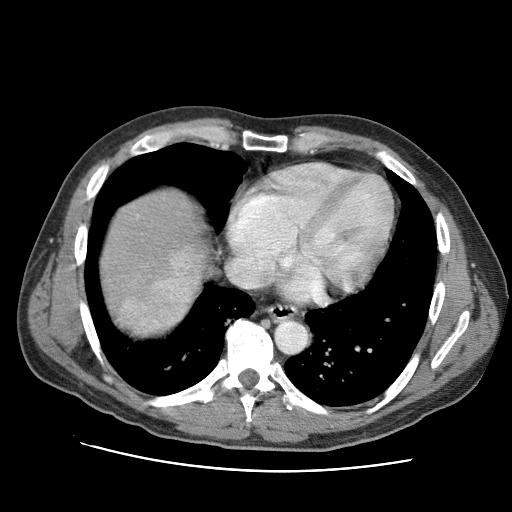
Contrast-enhanced abdominal CT (liver protocol), one axial slice; slice 88 of 95 in the series (ordered by position); reconstruction kernel STANDARD; 120 kVp; one of 2 acquisitions stored at this slice position; soft-tissue window (W 400 / L 40 HU); 2.5 mm slice thickness; 512 × 512 image matrix, field of view 360 × 360 mm. From the clinical record (not read from this slice): diagnosis: hepatocellular carcinoma (patient treated with transarterial chemoembolisation; whether this scan precedes or follows treatment is not stated here); TNM stage (as recorded): Stage-IVA; Child-Pugh class: A; tumour differentiation: moderately differentiated.
Outlined on this slice (semi-automatically segmented with operator editing):
- liver parenchyma outside the tumour (the mass and vessels are separate outlines, so this box may not span the whole liver): box from (x=100, y=190) to (x=204, y=326) px
- mass: (x=117, y=250)–(x=199, y=336)